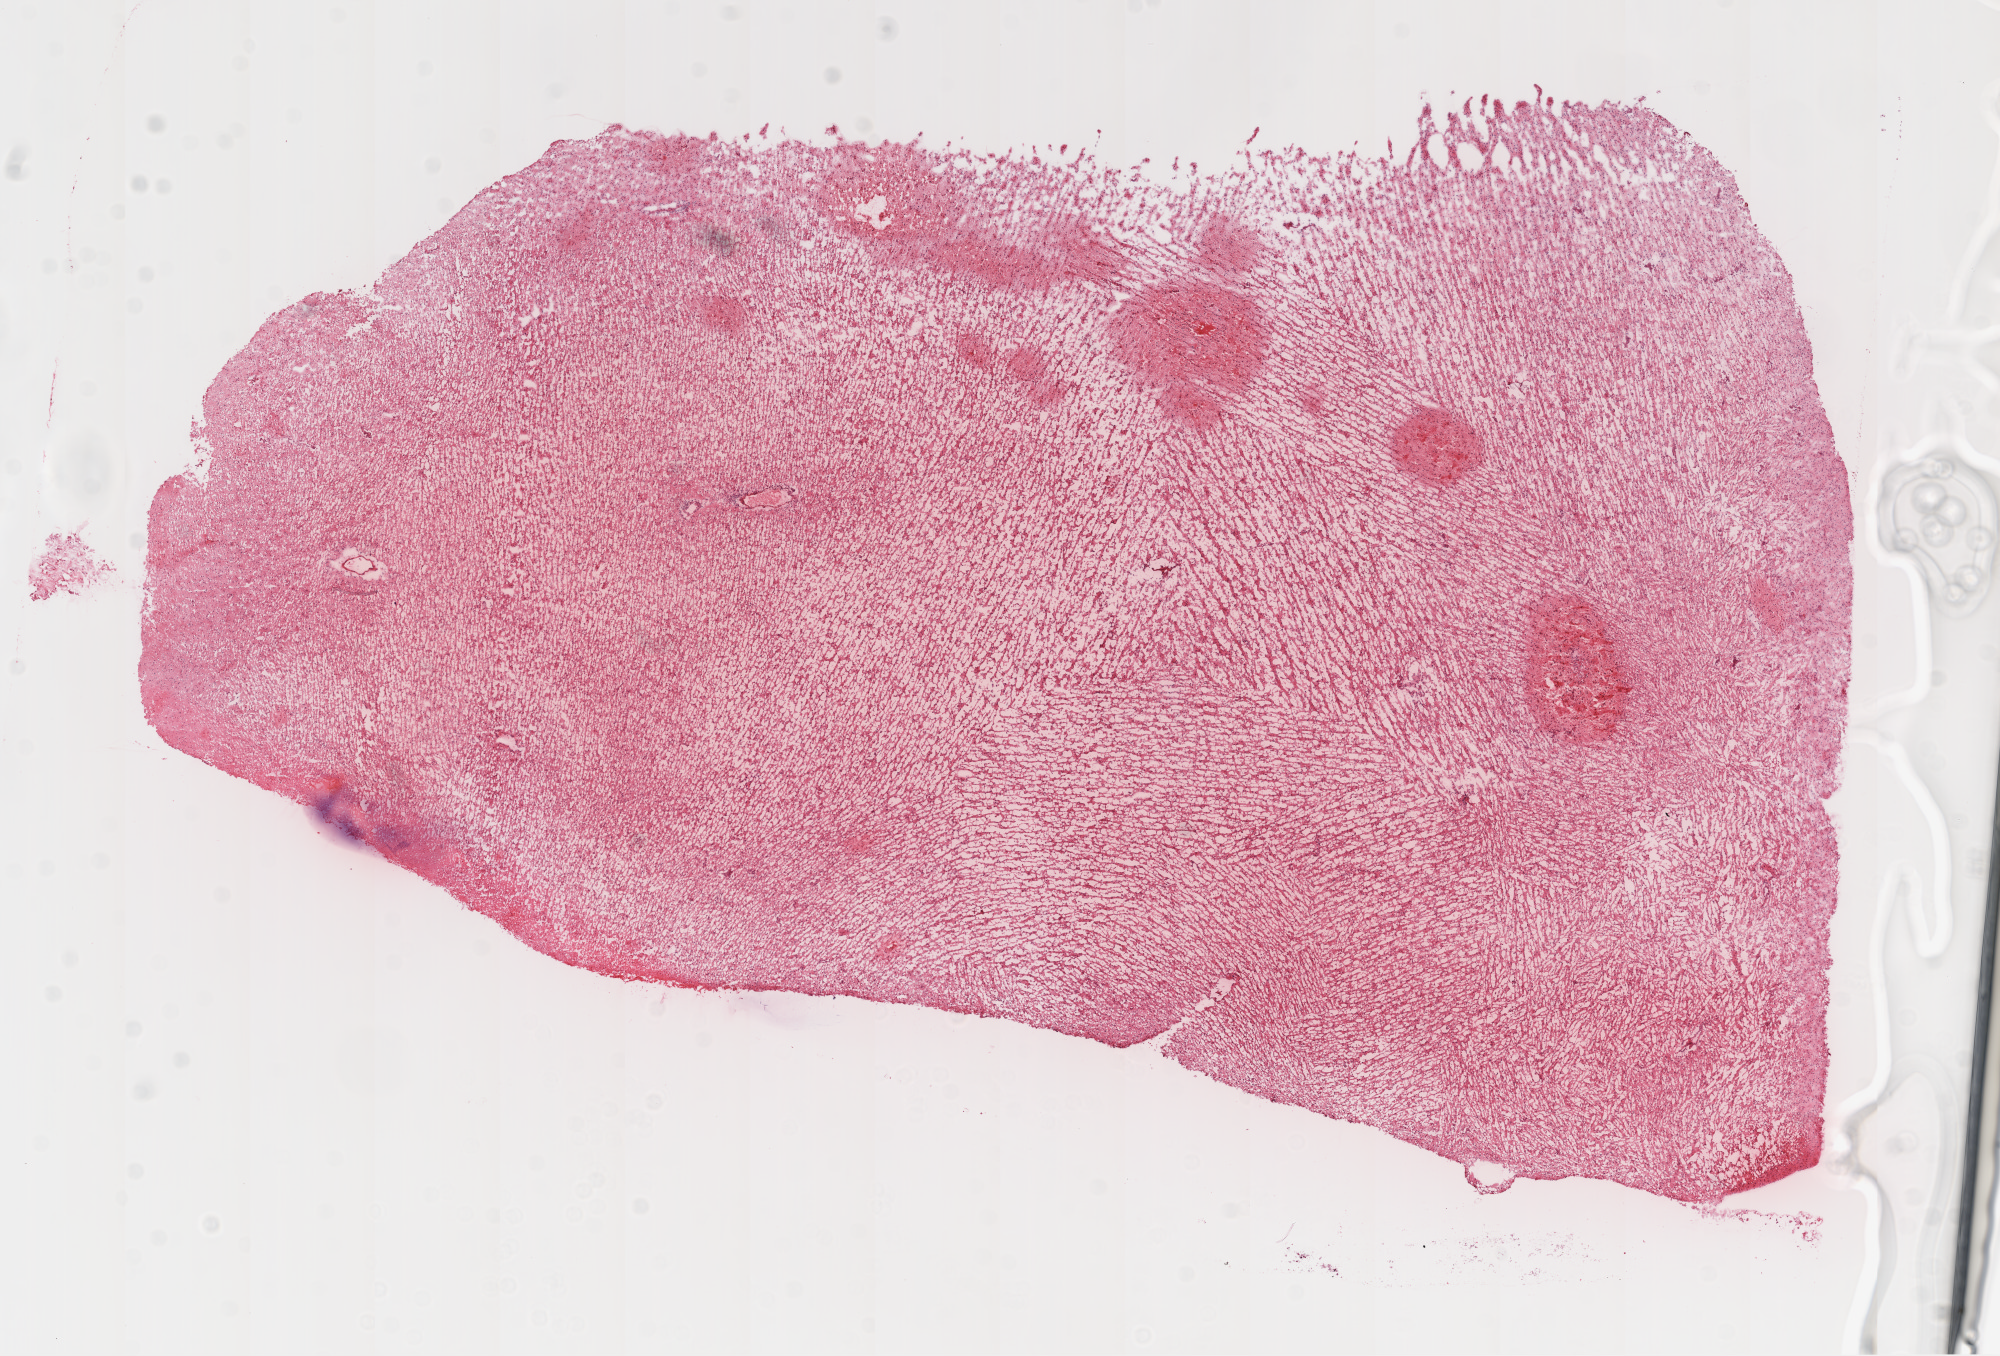
Whole-slide histology image, Hematoxylin and eosin (H&E) stained — whole scanned area (about 16.0 x 10.9 mm, acquisition: 20x scan) shown as a low-resolution overview. Frozen section. Brain, primary tumour sample. Male patient; age at initial diagnosis 77 years. Pathologist review of this section (percent, as recorded): tumour cells 100%, tumour nuclei 80%, normal cells 0%, stromal cells 0%, necrosis 0%.
Pathologic diagnosis: Glioblastoma.